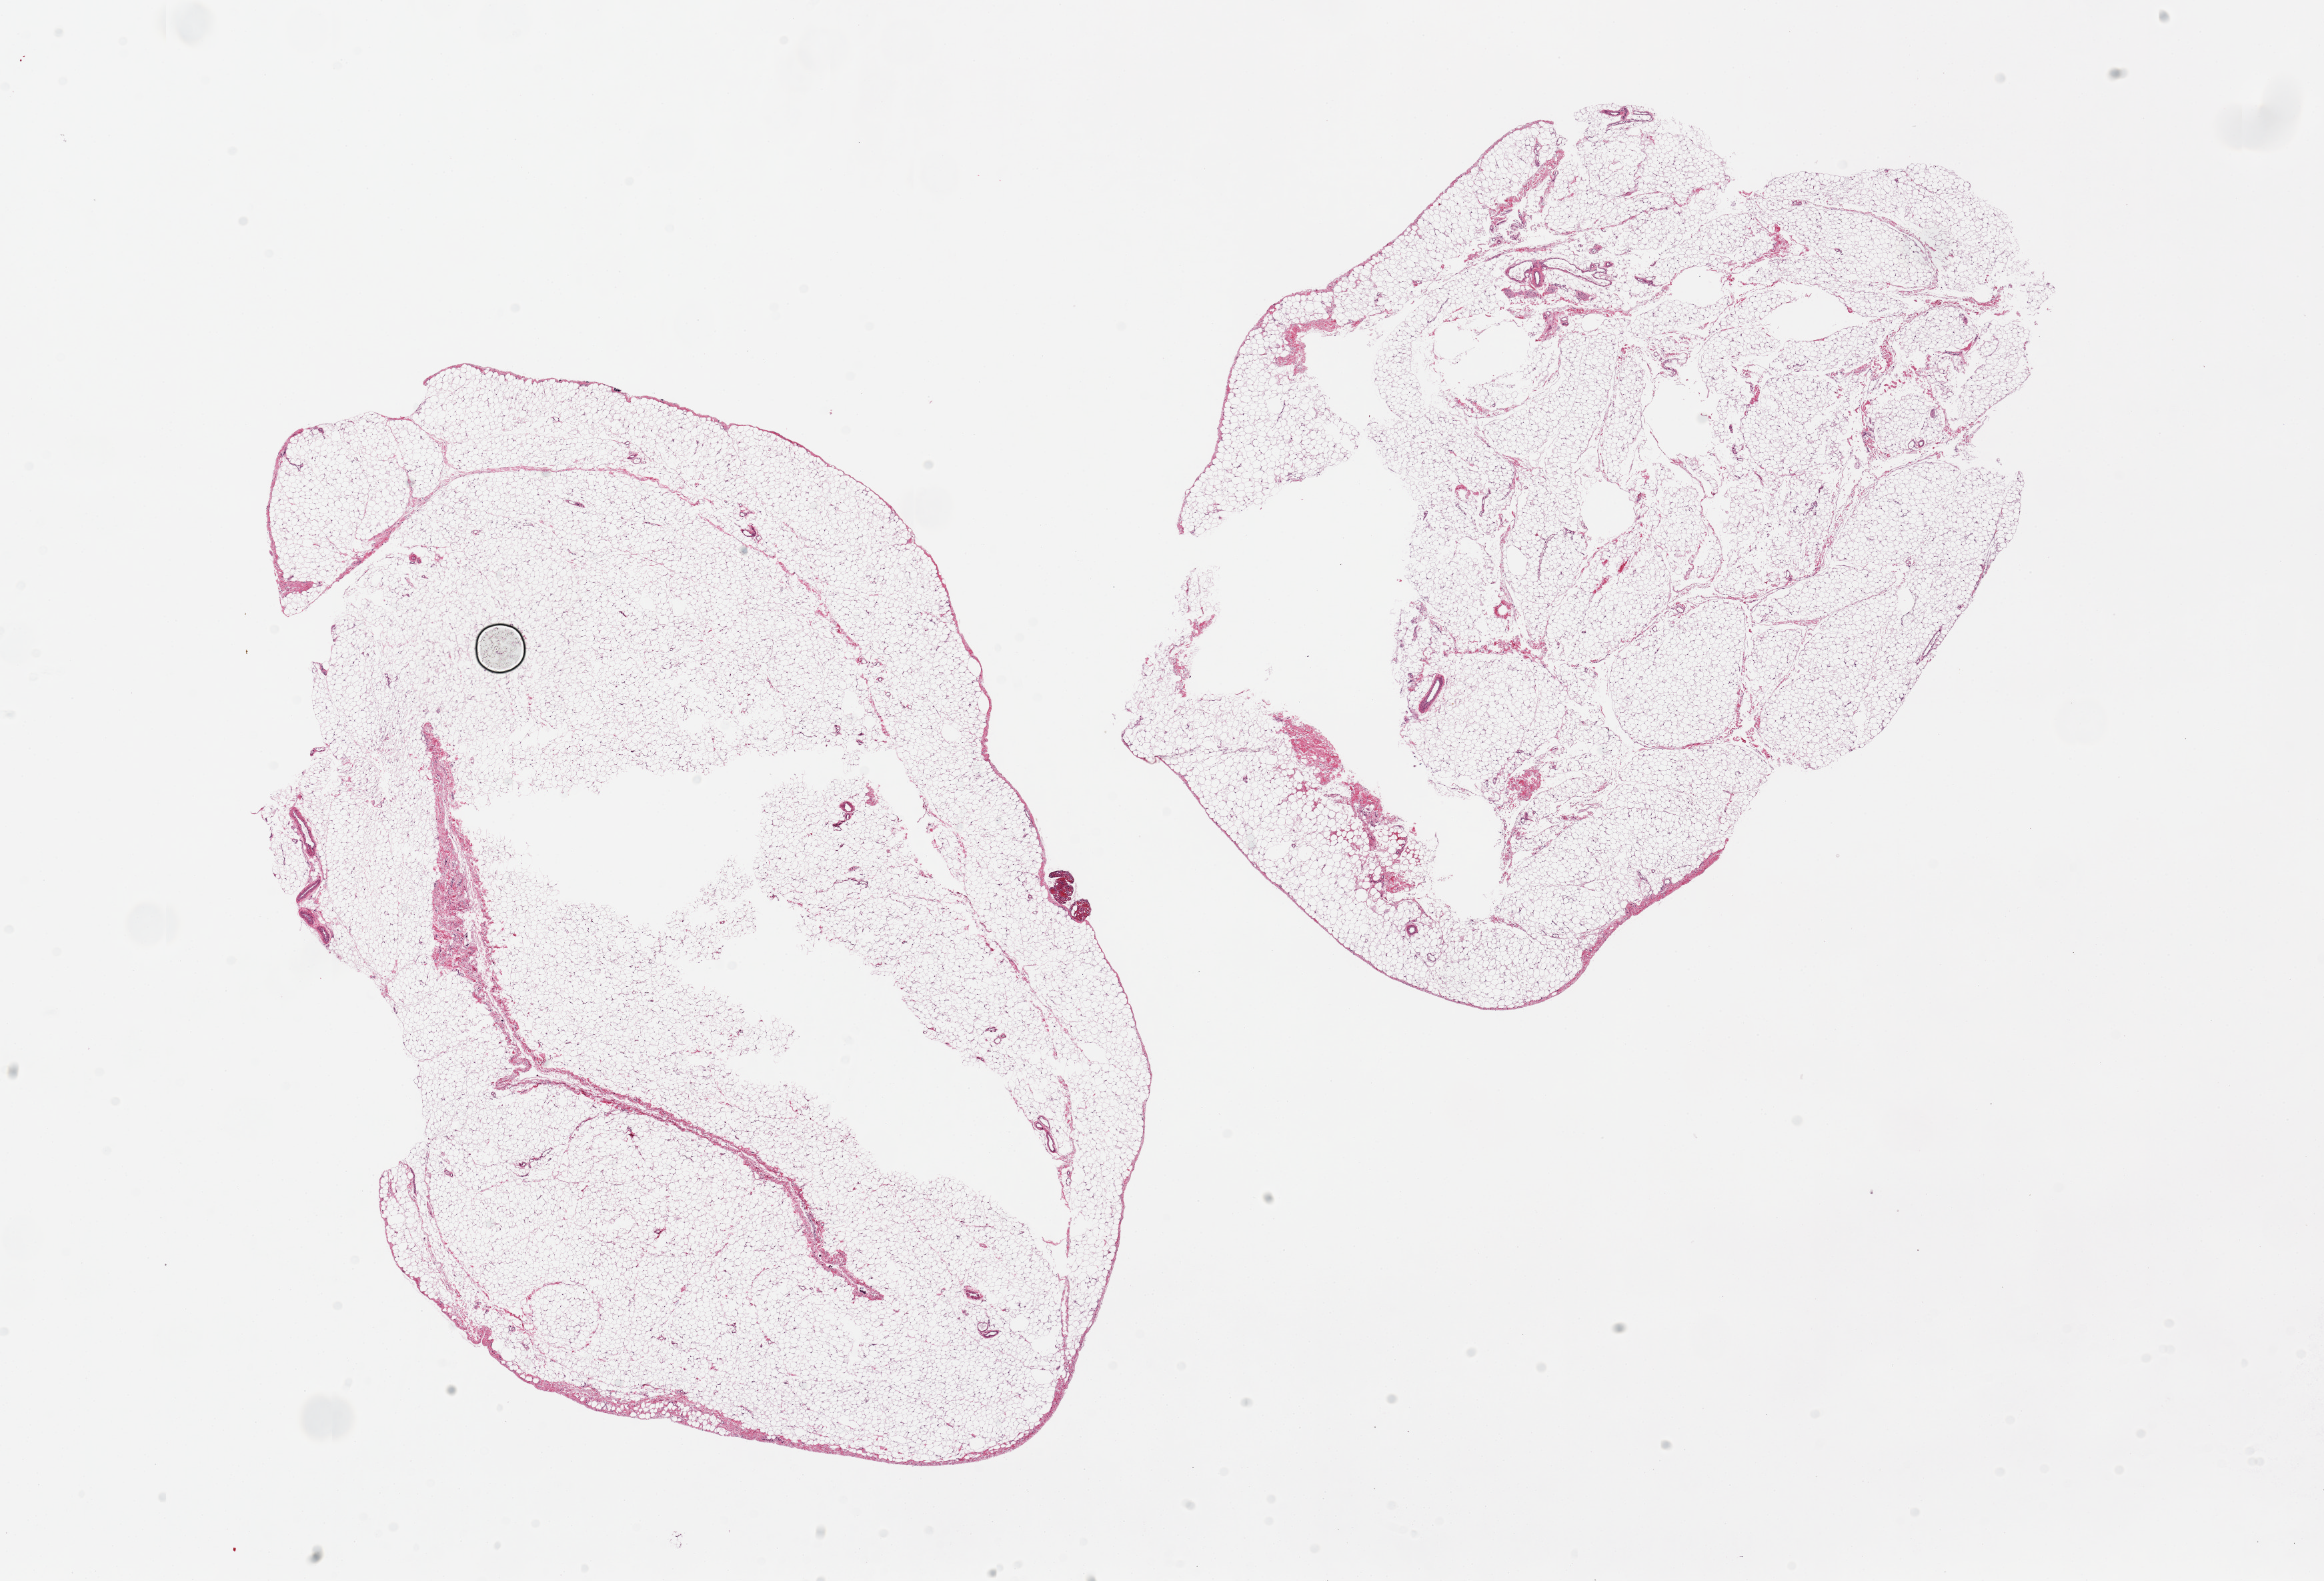
Haematoxylin and eosin whole-slide image — a low-resolution overview of the entire scanned area, about 27.6 x 18.8 mm; PAXgene-fixed paraffin-embedded (PFPE) section; section of omentum (target tissue); tissue donor sample. Donor sex: female.
Pathologist's review note for this sample: 2 pieces, 15x9 & 12x9mm: Central hollow defects in both pieces.